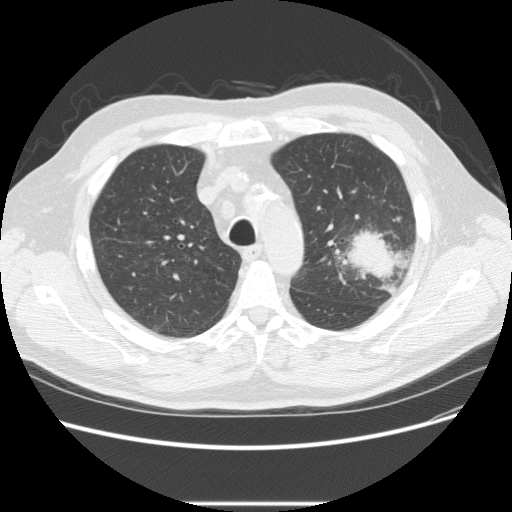
Low-dose screening chest CT, one axial slice; reconstruction kernel STANDARD; 120 kVp; lung window (W 1500 / L -600 HU); 512 × 512 image matrix.
Structures marked on this image (outlined manually by an expert reader):
- lesion 1 (tumor, upper lobe of left lung): bounding box <343,226,398,279> (left, top, right, bottom; pixels)